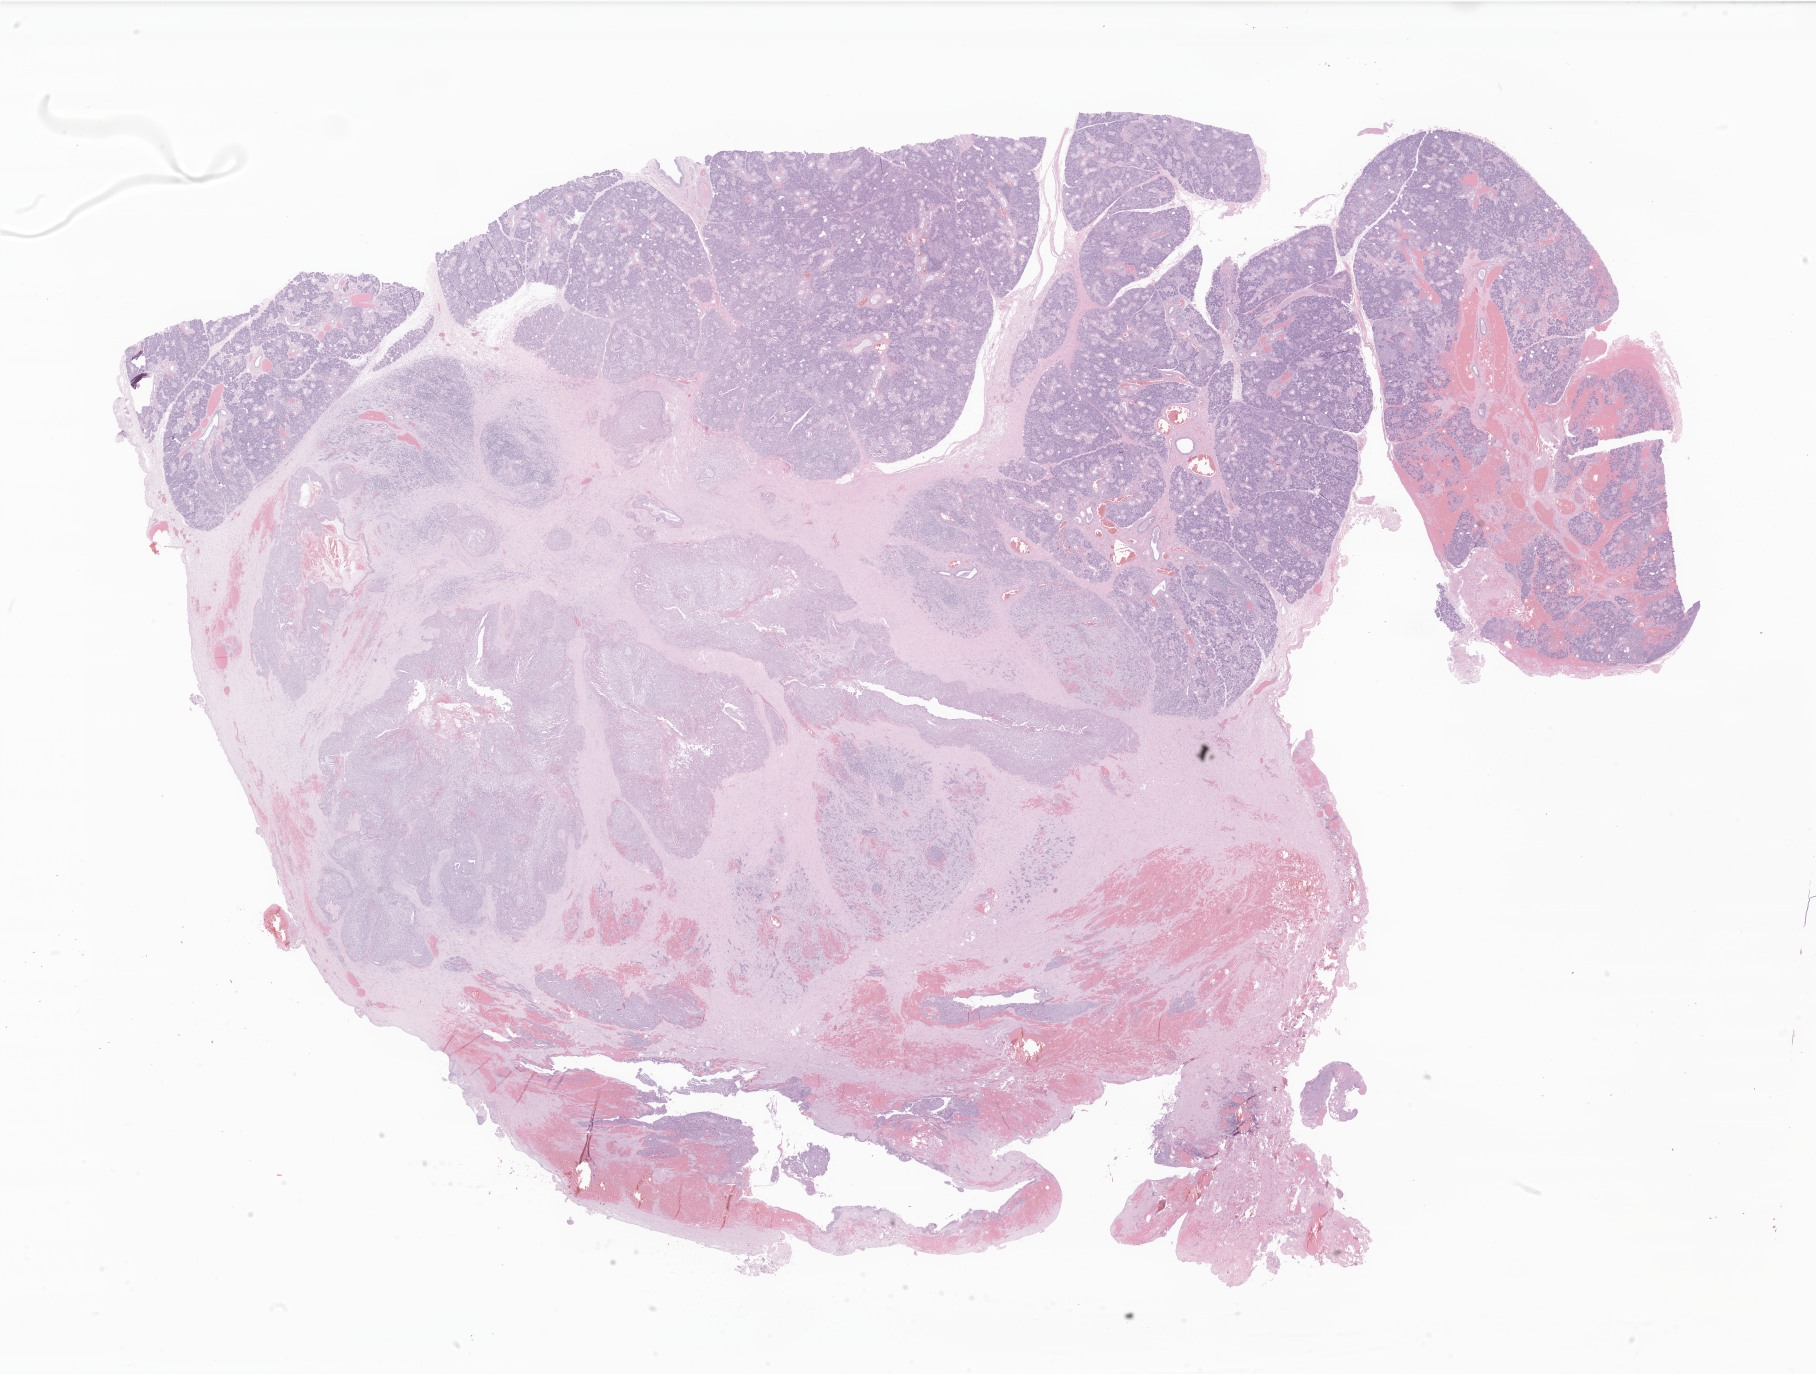
Haematoxylin and eosin whole-slide image of tumor tissue from the submandibular gland, a low-resolution overview of the entire scanned area, about 30.6 x 23.2 mm; formalin-fixed paraffin-embedded section. Patient male; age 195 months (16 years 3 months).
Recorded diagnosis: Mucoepidermoid carcinoma.